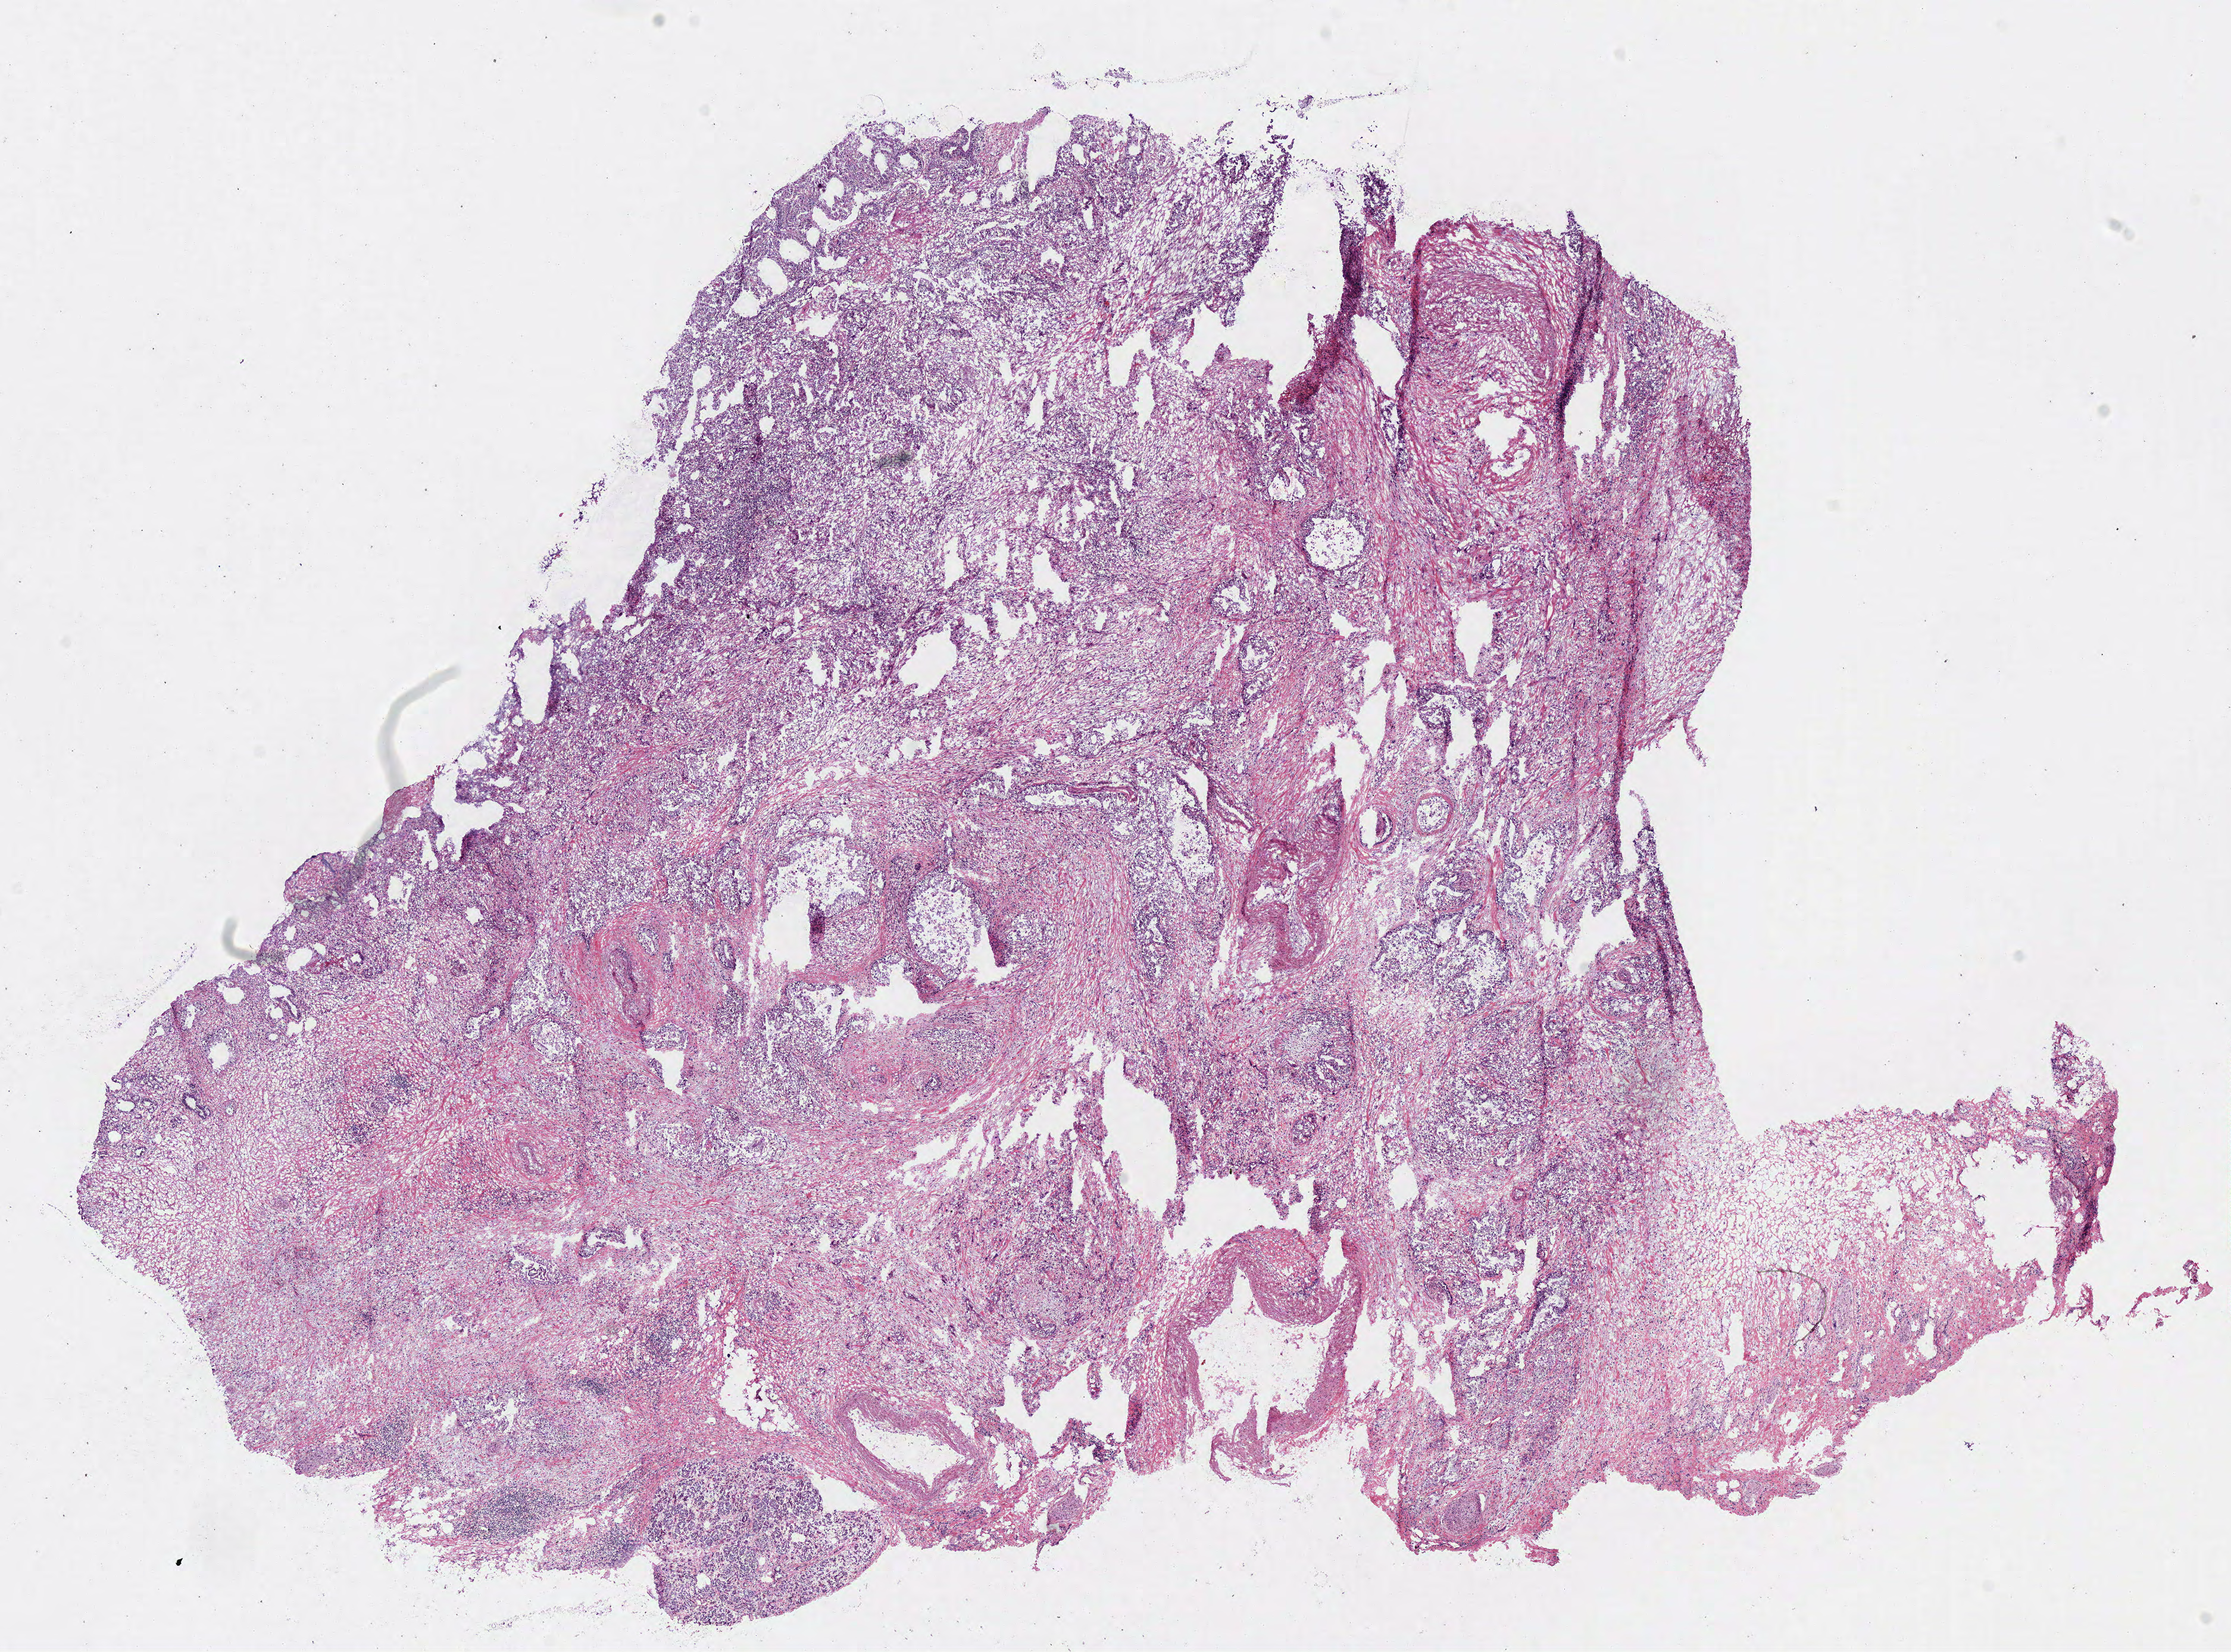
Digitized H&E-stained tissue section (whole slide), shown as a low-resolution overview of the whole scanned area (about 14.8 x 10.9 mm, from a 40x scan). Frozen section from the bottom of the tissue portion. Primary tumour sample from the pancreas. Female patient; age at initial diagnosis 85 years. Histologic grade: GX (grade cannot be assessed). Composition of this section per pathologist review: tumour cells 67%, tumour nuclei 70%, normal cells 3%, stromal cells 30%, necrosis 0%.
* histologic diagnosis: Infiltrating duct carcinoma, NOS (head of pancreas)
* AJCC pathologic stage: IIB (6th edition)
* lymph nodes positive (case pathology): 1 of 10 examined